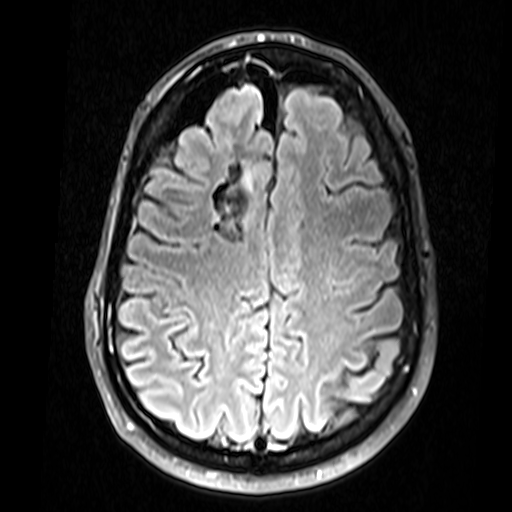
Brain MRI from a brain-tumour surgery series, one axial slice. Slice 46 of 74 in the series (ordered by position). T2 FLAIR. 512 × 512 image matrix. From the clinical record (not read from this slice): histopathology: Glial fibroma; tumour location: Right Frontal.
Annotated regions visible in this slice (expert manual segmentation):
- residual tumour: bounding box (x1, y1, x2, y2) in pixels: (241, 169, 252, 190)